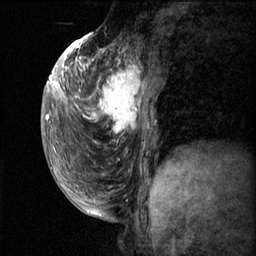
Breast MRI (dynamic contrast-enhanced), one sagittal slice. Slice 25 of 60 in the series (ordered by position). Dynamic contrast-enhanced series, image 2 of 3 at this slice position (ordered by acquisition). 1.5 T. TE 4.2 ms, TR 11.1 ms. 2 mm slice thickness. 256 × 256 image matrix, field of view 180 × 180 mm. Patient: female, 50 years.
Structures marked on this image (semi-automatic segmentation, software-assisted and operator-edited):
- analysis volume of interest (the breast-tissue region the enhancement analysis was run in; not a lesion): bounding box [x1, y1, x2, y2] px = [82, 56, 164, 143]
- tumour enhancement mask (voxels above the 70 % enhancement threshold inside the analysis volume of interest): [82, 58, 149, 135]